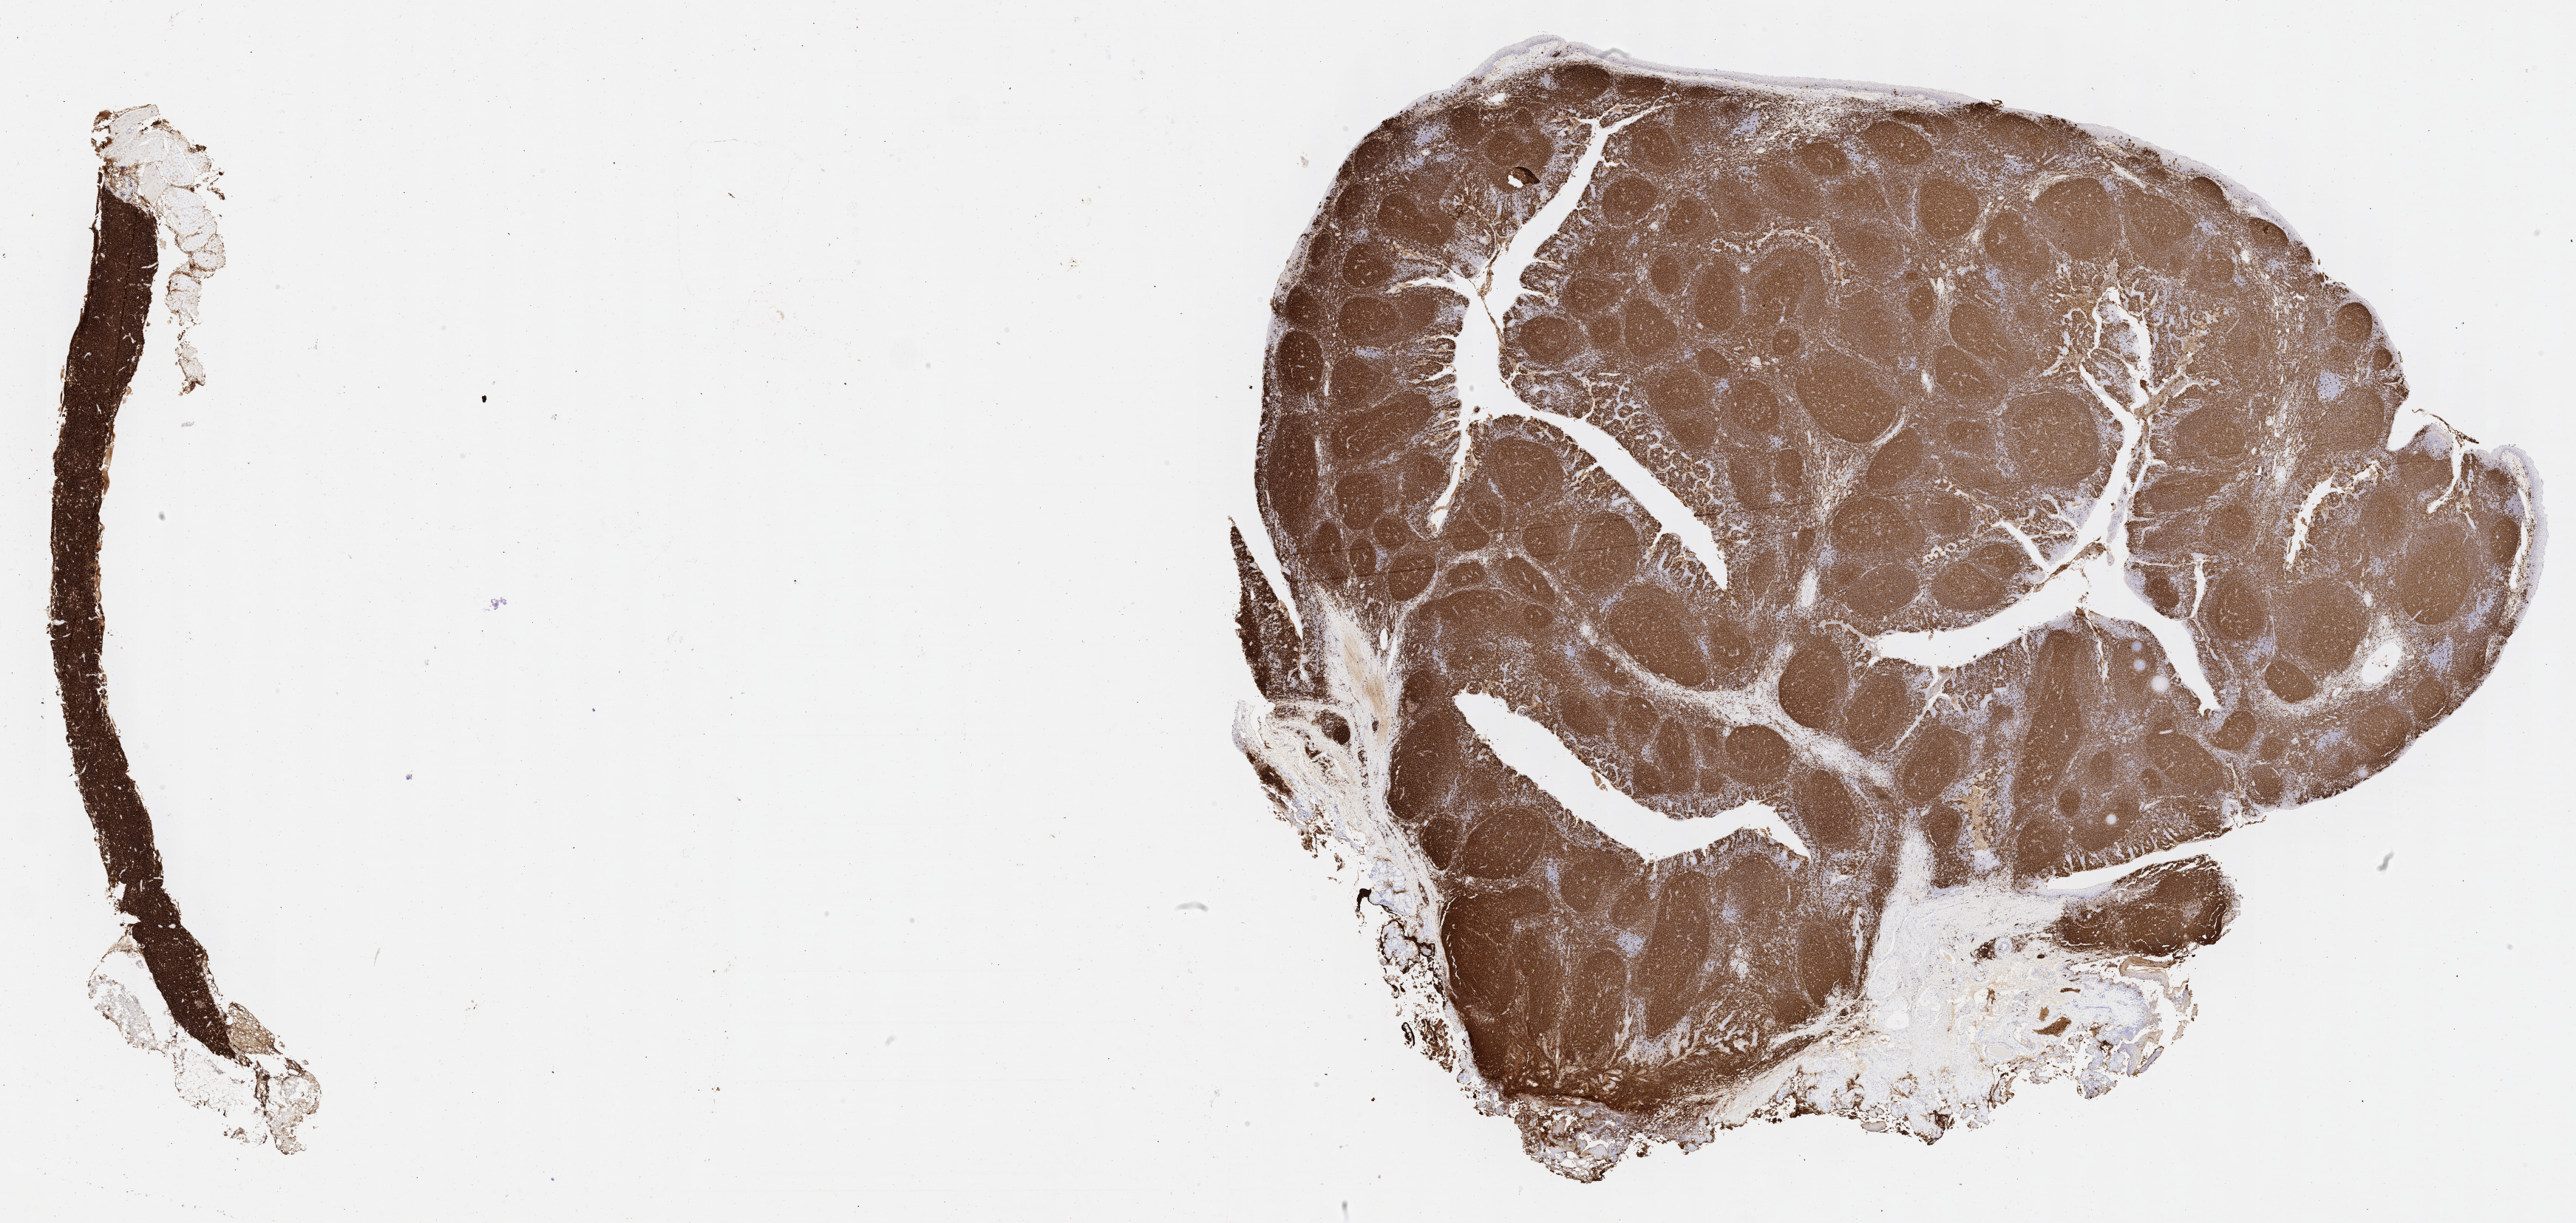
Immunohistochemistry (IHC) whole-slide image stained for CD20, shown as a low-resolution overview of the whole scanned area (about 28.2 x 13.4 mm); tumor tissue; anatomic site: cranium. Female patient; age at initial diagnosis 7 years.
Diagnosis: Burkitt lymphoma, NOS.